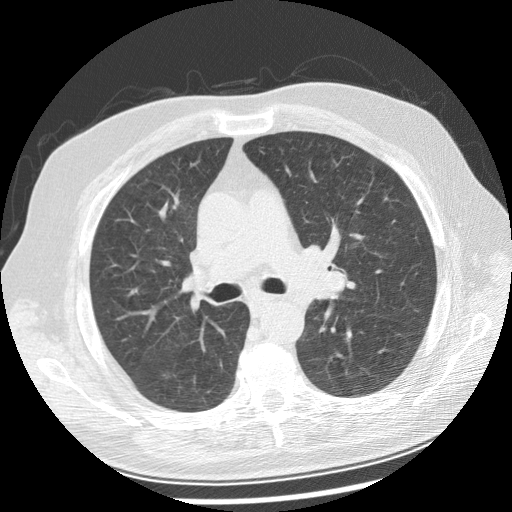
Axial slice from a low-dose chest CT screening exam. Baseline screening round. Lung window (W 1500 / L -600 HU). 120 kVp. 512 × 512 image matrix, field of view 360 × 360 mm. Male participant, aged 70 years at enrolment.
Expert reader's lesion annotation, bounding box <278,242,360,305> (left, top, right, bottom; pixels). Screening reader's record for this exam: no non-calcified nodule ≥4 mm recorded. Lung cancer was diagnosed 29 days after this screen: squamous cell carcinoma, keratinizing, NOS, left main stem bronchus, moderately differentiated (G2), stage IIIB (AJCC 6th edition), 40 mm at pathology.